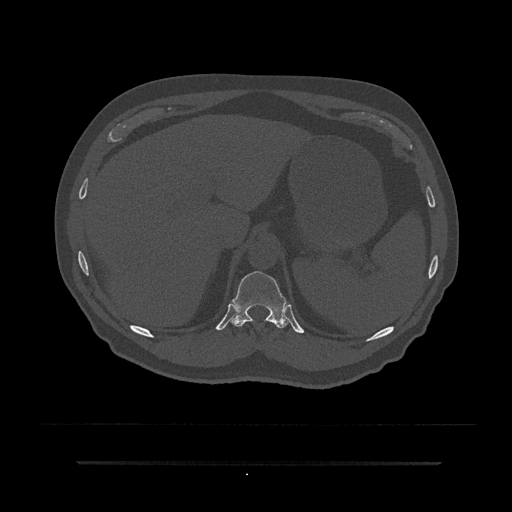
CT including the spine, one axial slice; position 283 of 797 along the scan axis; 120 kVp; bone window (W 1800 / L 400 HU); 512 × 512 image matrix, field of view 464 × 464 mm. Patient: male, 59 years. From the clinical record (not read from this slice): primary cancer: bile ducts; vertebrae with lytic lesions (as recorded): T10.
Annotated regions visible in this slice (semi-automatic segmentation, software-assisted and operator-edited):
- T11 vertebra: bounding box <230,271,291,329> (left, top, right, bottom; pixels)